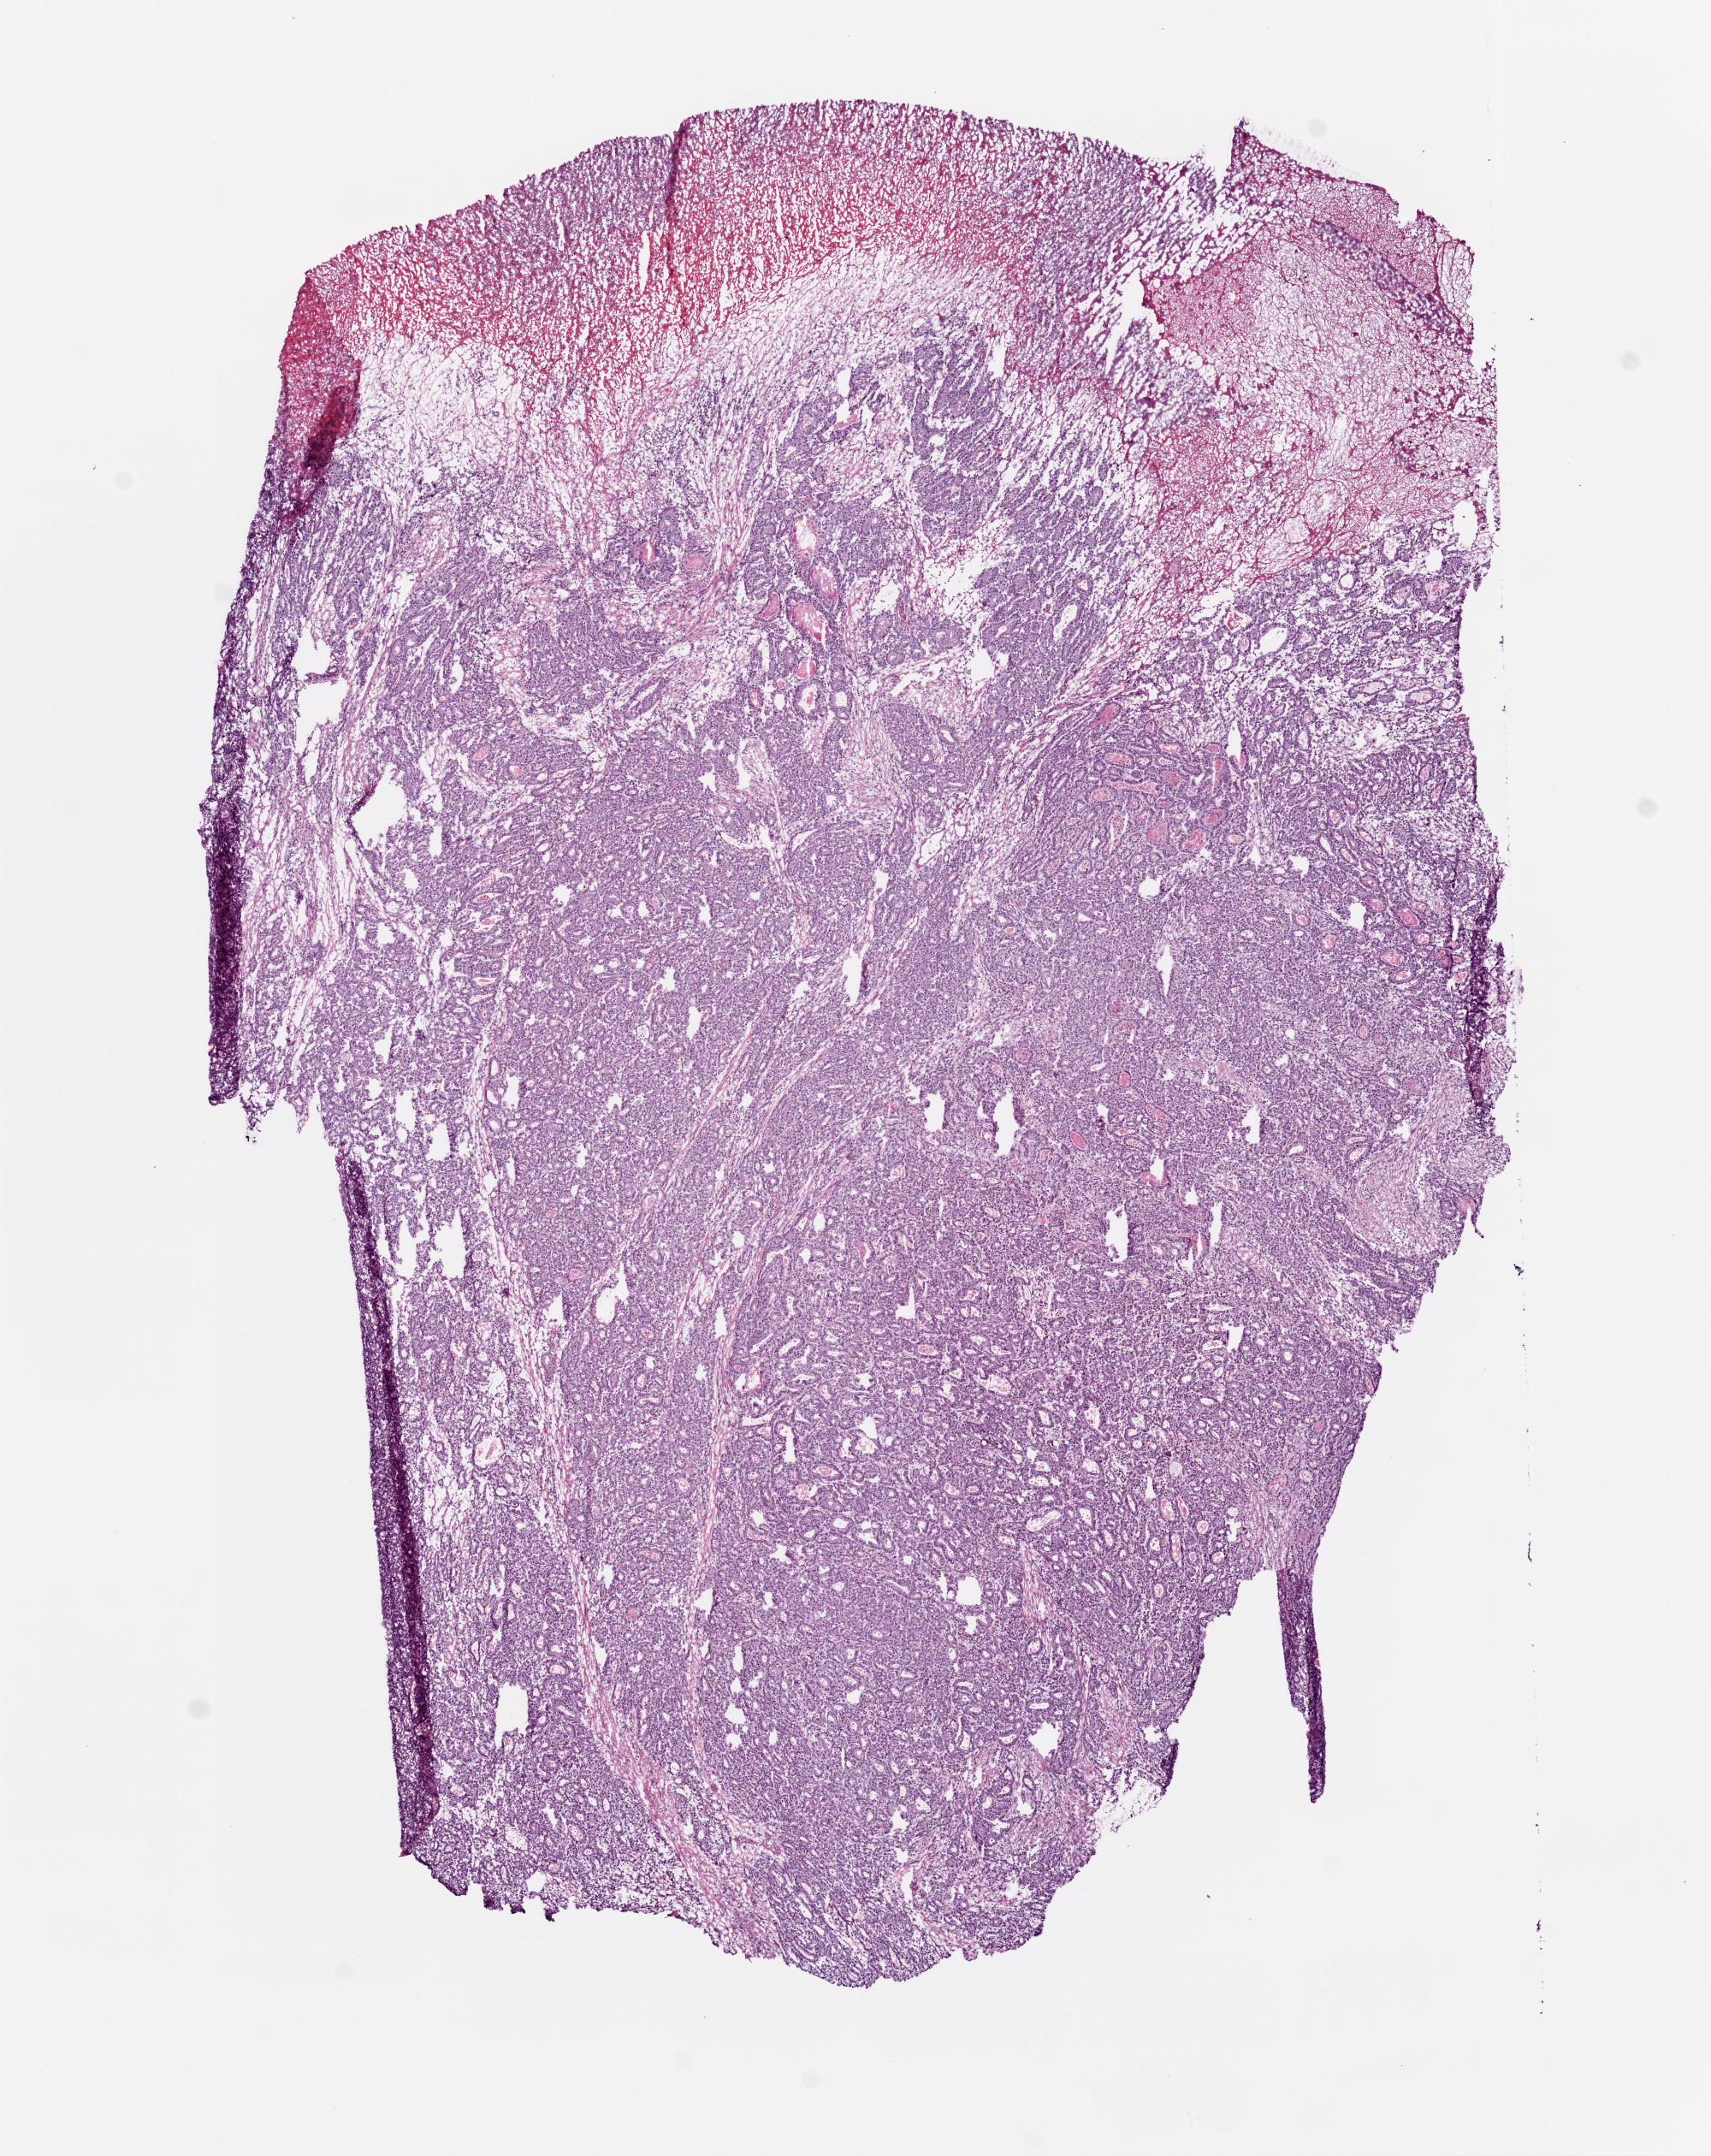
Digitized H&E tissue section (whole slide), low-resolution overview of the scanned area, about 8.0 x 10.1 mm (acquisition: 20x scan); frozen section from the bottom of the tissue portion; sample: primary tumour, stomach. Female, age 78 years at initial diagnosis. Histologic grade: G2 (moderately differentiated). Slide review estimates, as recorded: tumour cells 80%, tumour nuclei 80%, normal cells 0%, stromal cells 10%, necrosis 10%.
• pathologic diagnosis: Adenocarcinoma, intestinal type (body of stomach)
• AJCC pathologic stage: II (6th edition)
• lymph nodes positive (case pathology): 3 of 39 examined